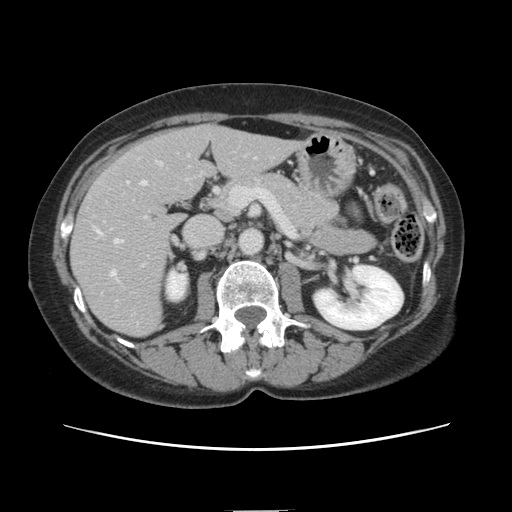
Contrast-enhanced abdominal CT, one axial slice. Position 62 of 141 along the scan axis. 120 kVp. Intravenous contrast given. Soft-tissue window (W 400 / L 40 HU). 2.5 mm slice thickness. 512 × 512 image matrix, field of view 350 × 350 mm. Female patient, age 63 years. Case-level facts recorded for this patient, not image findings: diagnosis: colorectal cancer liver metastases, imaged before liver resection; multiple liver metastases: yes; largest metastasis: 3.2 cm; disease in both lobes: yes.
Annotated regions visible in this slice (manually delineated by an expert):
- hepatic veins: bounding box <97,163,161,278> (left, top, right, bottom; pixels)
- liver: <72,126,297,336>
- planned liver remnant (the part of the liver to remain after resection): <176,125,297,189>
- portal vein (with intrahepatic branches): <115,161,159,243>